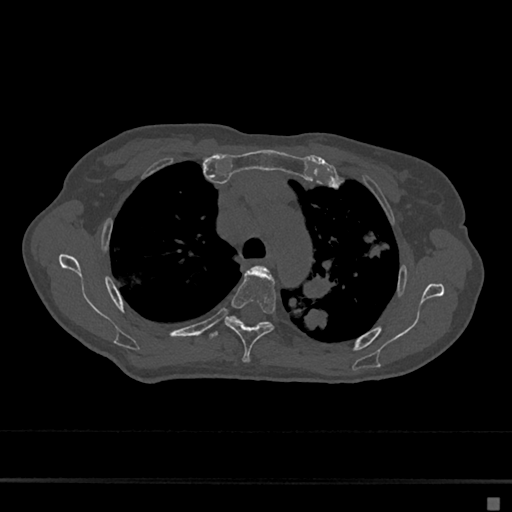
CT including the spine, one axial slice. Slice 495 of 797 in the series (ordered by position). 120 kVp. Bone window (W 1800 / L 400 HU). 0.5 mm slice thickness. 512 × 512 image matrix, field of view 360 × 360 mm. Patient: female, 68 years. From the clinical record (not read from this slice): primary cancer: renal.
Annotated regions visible in this slice (semi-automatically segmented with operator editing):
- T3 vertebra: bounding box [x1, y1, x2, y2] px = [261, 267, 265, 271]
- T4 vertebra: [224, 271, 276, 363]
- T5 vertebra: [209, 315, 271, 339]